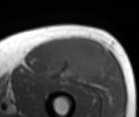
MRI of an extremity soft-tissue mass, one axial slice. Slice 44 of 86 in the series (ordered by position). MR volume resampled by the dataset authors to the PET/CT grid (not the native acquisition matrix). 139 × 117 image matrix, field of view 136 × 114 mm. Male patient. Case-level facts recorded for this patient, not image findings: histological type: extraskeletal osteosarcoma; grade: high; site of the primary tumour: thigh.
Annotated regions visible in this slice (expert contour drawn on MRI and transferred to this co-registered scan by the dataset authors):
- gross tumour volume (mass): bounding box [x1, y1, x2, y2] px = [54, 37, 103, 79]